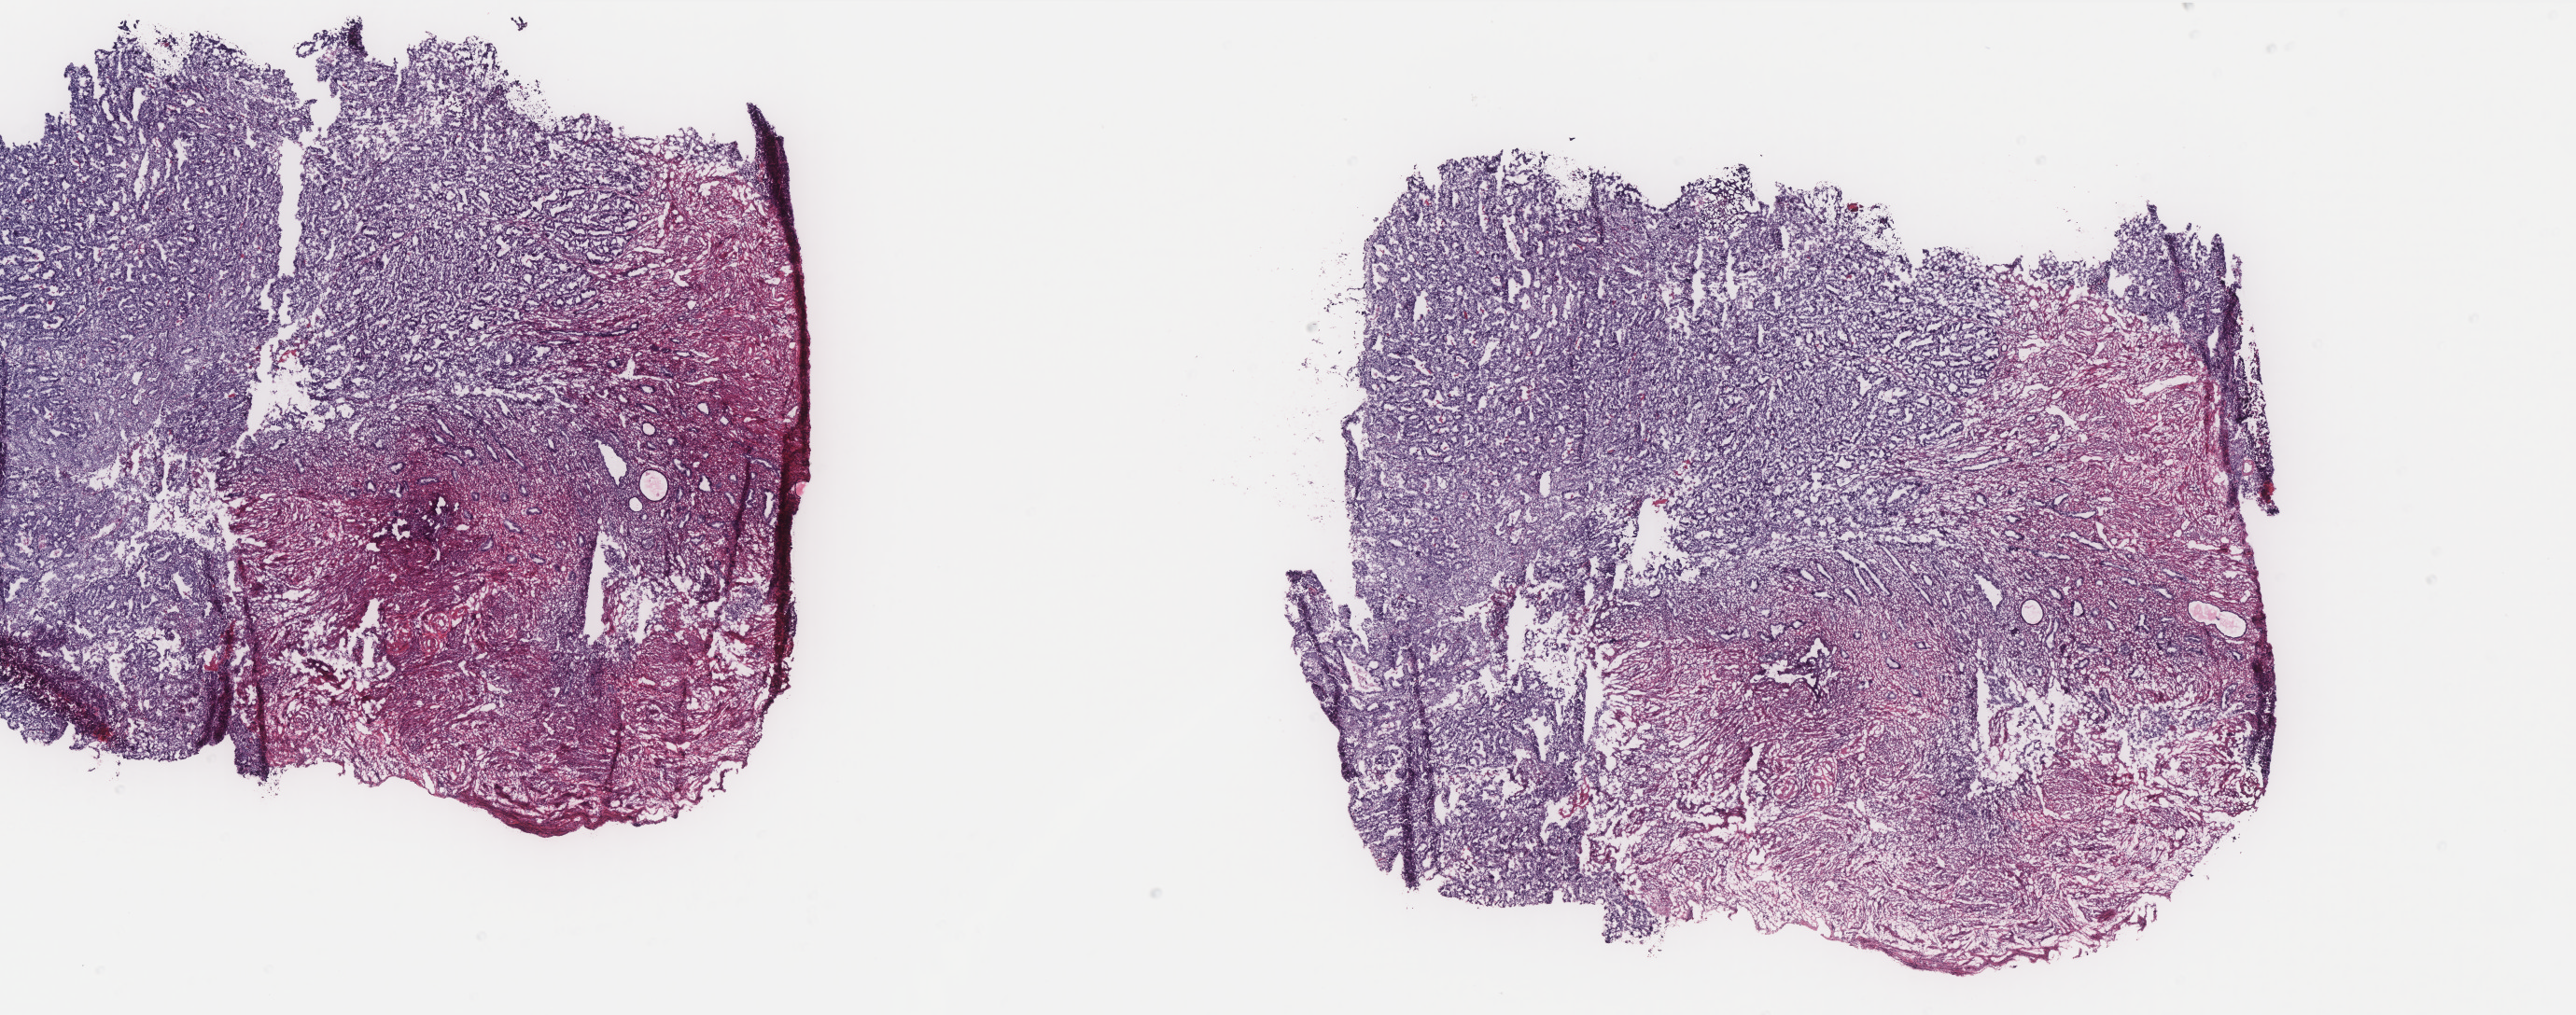
H&E-stained whole-slide image, a low-resolution overview of the entire scanned area, about 22.1 x 8.7 mm (slide scanned at 40x). Frozen section. Sample: primary tumour, uterus. Patient: female, age at initial diagnosis 68 years. Histologic grade: G2 (moderately differentiated). Slide review estimates, as recorded: tumour cells 25%, tumour nuclei 15%, normal cells 59%, stromal cells 15%, necrosis 1%. Infiltration values recorded for this section: lymphocyte infiltration 5%, monocyte infiltration 0%, neutrophil infiltration 0%.
* diagnosis: Endometrioid adenocarcinoma, NOS (endometrium)
* FIGO stage: IIB